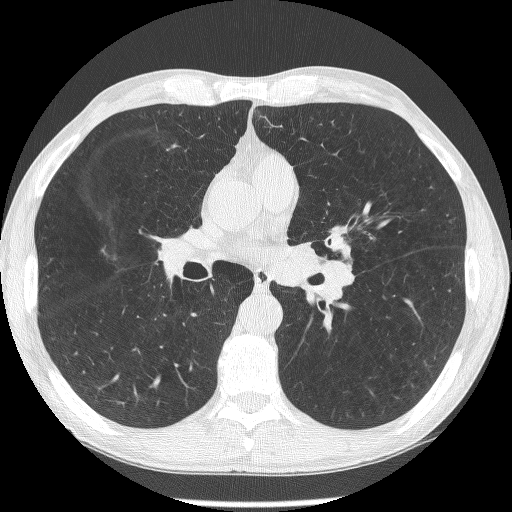
Low-dose screening chest CT, axial slice; second annual screen; lung window (W 1500 / L -600 HU); 1.25 mm slice thickness; 120 kVp; slice 147 of 293 in the series; 512 × 512 image matrix, field of view 326 × 326 mm. Male participant, aged 62 years at enrolment.
- Expert-annotated lung lesion, bounding box (x1, y1, x2, y2) in pixels: (317, 217, 367, 266).
- The screening reader recorded 2 non-calcified nodules or masses ≥4 mm on this exam (lingula, lingula); which of them this box marks is not recorded.
- Official screen result: positive, other.
- Later outcome: lung cancer diagnosed 95 days after this screen — small cell carcinoma, NOS, left upper lobe, stage IIIA (AJCC 6th edition).